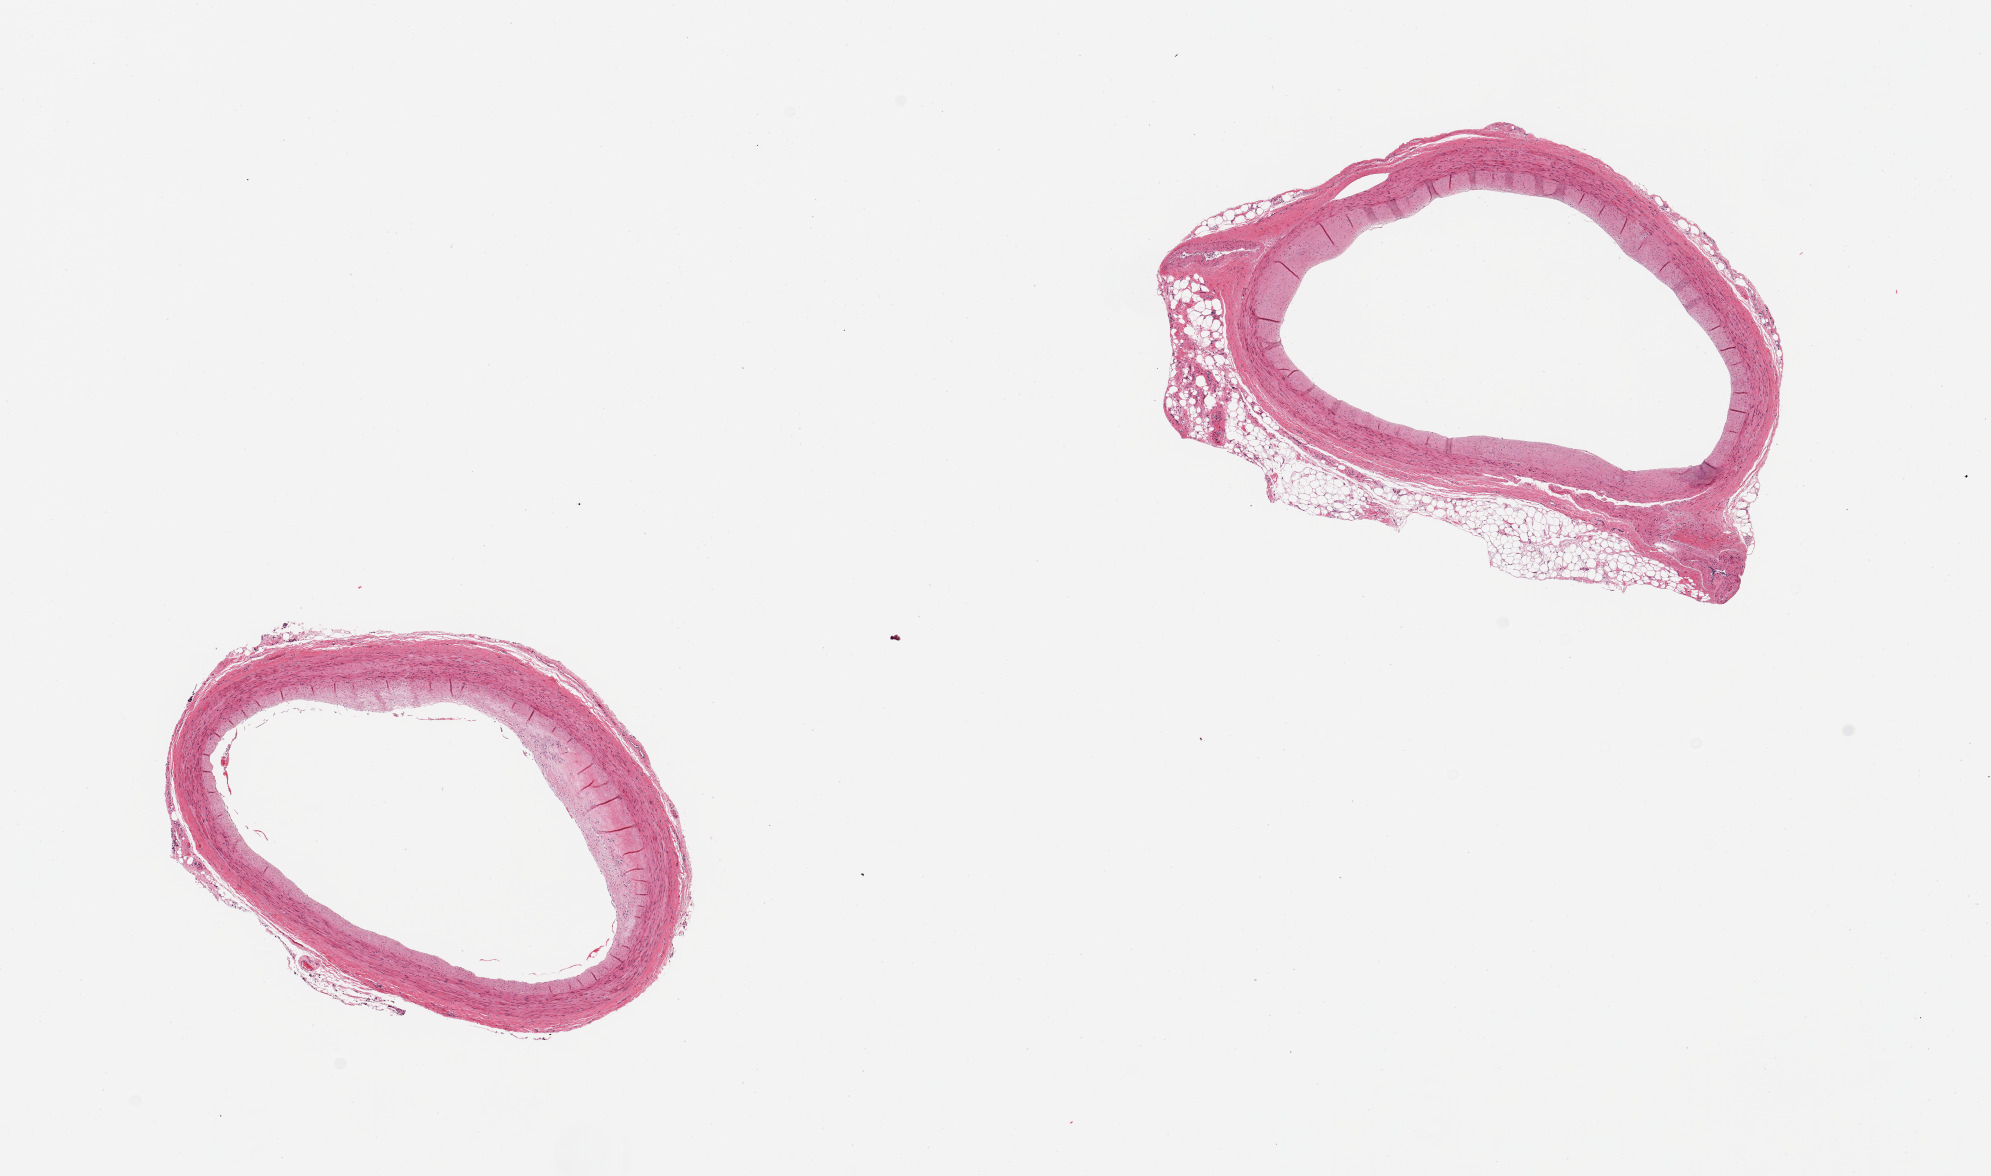
Whole-slide image, H&E stain, whole scanned area (about 15.8 x 9.3 mm) shown as a low-resolution overview, PAXgene-fixed, paraffin-embedded tissue, section of coronary artery (target tissue), tissue donor sample. Donor: male.
Review note (as recorded): 2 pieces, mild atherosclerosis, partial peripheral rim of fat (~30% of one piece).